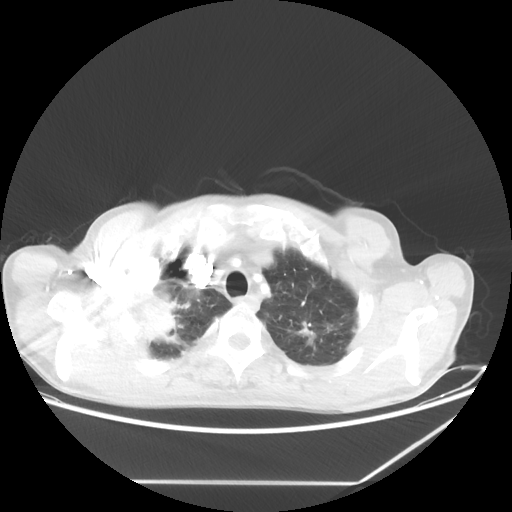
Chest CT, one axial slice; slice 56 of 65 in the series (ordered by position); reconstruction kernel STANDARD; lung window (W 1500 / L -600 HU); 5 mm slice thickness; 512 × 512 image matrix, field of view 397 × 397 mm. Patient: male, 68 years. From the clinical record (not read from this slice): clinical TNM (as recorded): T3 N3 M0.
Annotated regions visible in this slice (rectangle marked by the reading radiologist):
- lung tumour (recorded histology: adenocarcinoma): box from (x=133, y=288) to (x=187, y=348) px